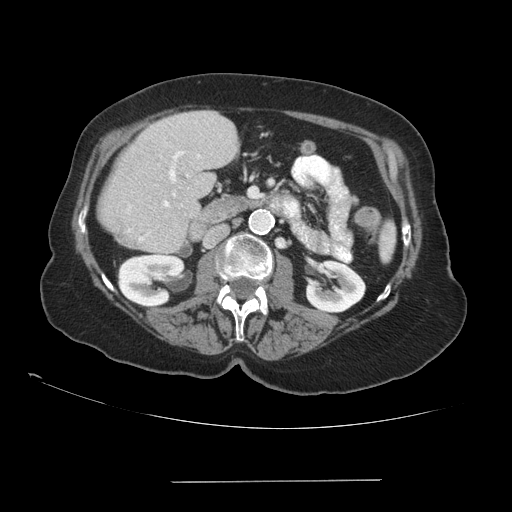
Contrast-enhanced abdominal CT (liver protocol), one axial slice. Slice 36 of 89 in the series (ordered by position). Soft-tissue window (W 400 / L 40 HU). 512 × 512 image matrix, field of view 400 × 400 mm. Case-level facts recorded for this patient, not image findings: diagnosis: hepatocellular carcinoma (patient treated with transarterial chemoembolisation; whether this scan precedes or follows treatment is not stated here); TNM stage (as recorded): Stage-IVA; Child-Pugh class: A; tumour differentiation: poorly differentiated; tumour nodularity: uninodular.
Structures marked on this image (semi-automatic segmentation, software-assisted and operator-edited):
- liver parenchyma outside the tumour (the mass and vessels are separate outlines, so this box may not span the whole liver): bounding box <100,110,238,250> (left, top, right, bottom; pixels)
- liver vessels: <139,151,200,241>